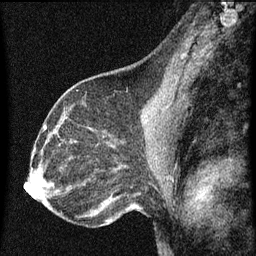
Breast MRI (dynamic contrast-enhanced), one sagittal slice; slice 36 of 60 in the series (ordered by position); dynamic contrast-enhanced series, image 2 of 3 at this slice position (ordered by acquisition); 1.5 T; TE 4.2 ms, TR 8 ms; 2 mm slice thickness; 256 × 256 image matrix, field of view 180 × 180 mm. Patient: female, 43 years.
Structures marked on this image (semi-automatically segmented with operator editing):
- analysis volume of interest (the breast-tissue region the enhancement analysis was run in; not a lesion): box from (x=53, y=104) to (x=101, y=151) px
- tumour enhancement mask (voxels above the 70 % enhancement threshold inside the analysis volume of interest): (x=75, y=130)–(x=93, y=143)